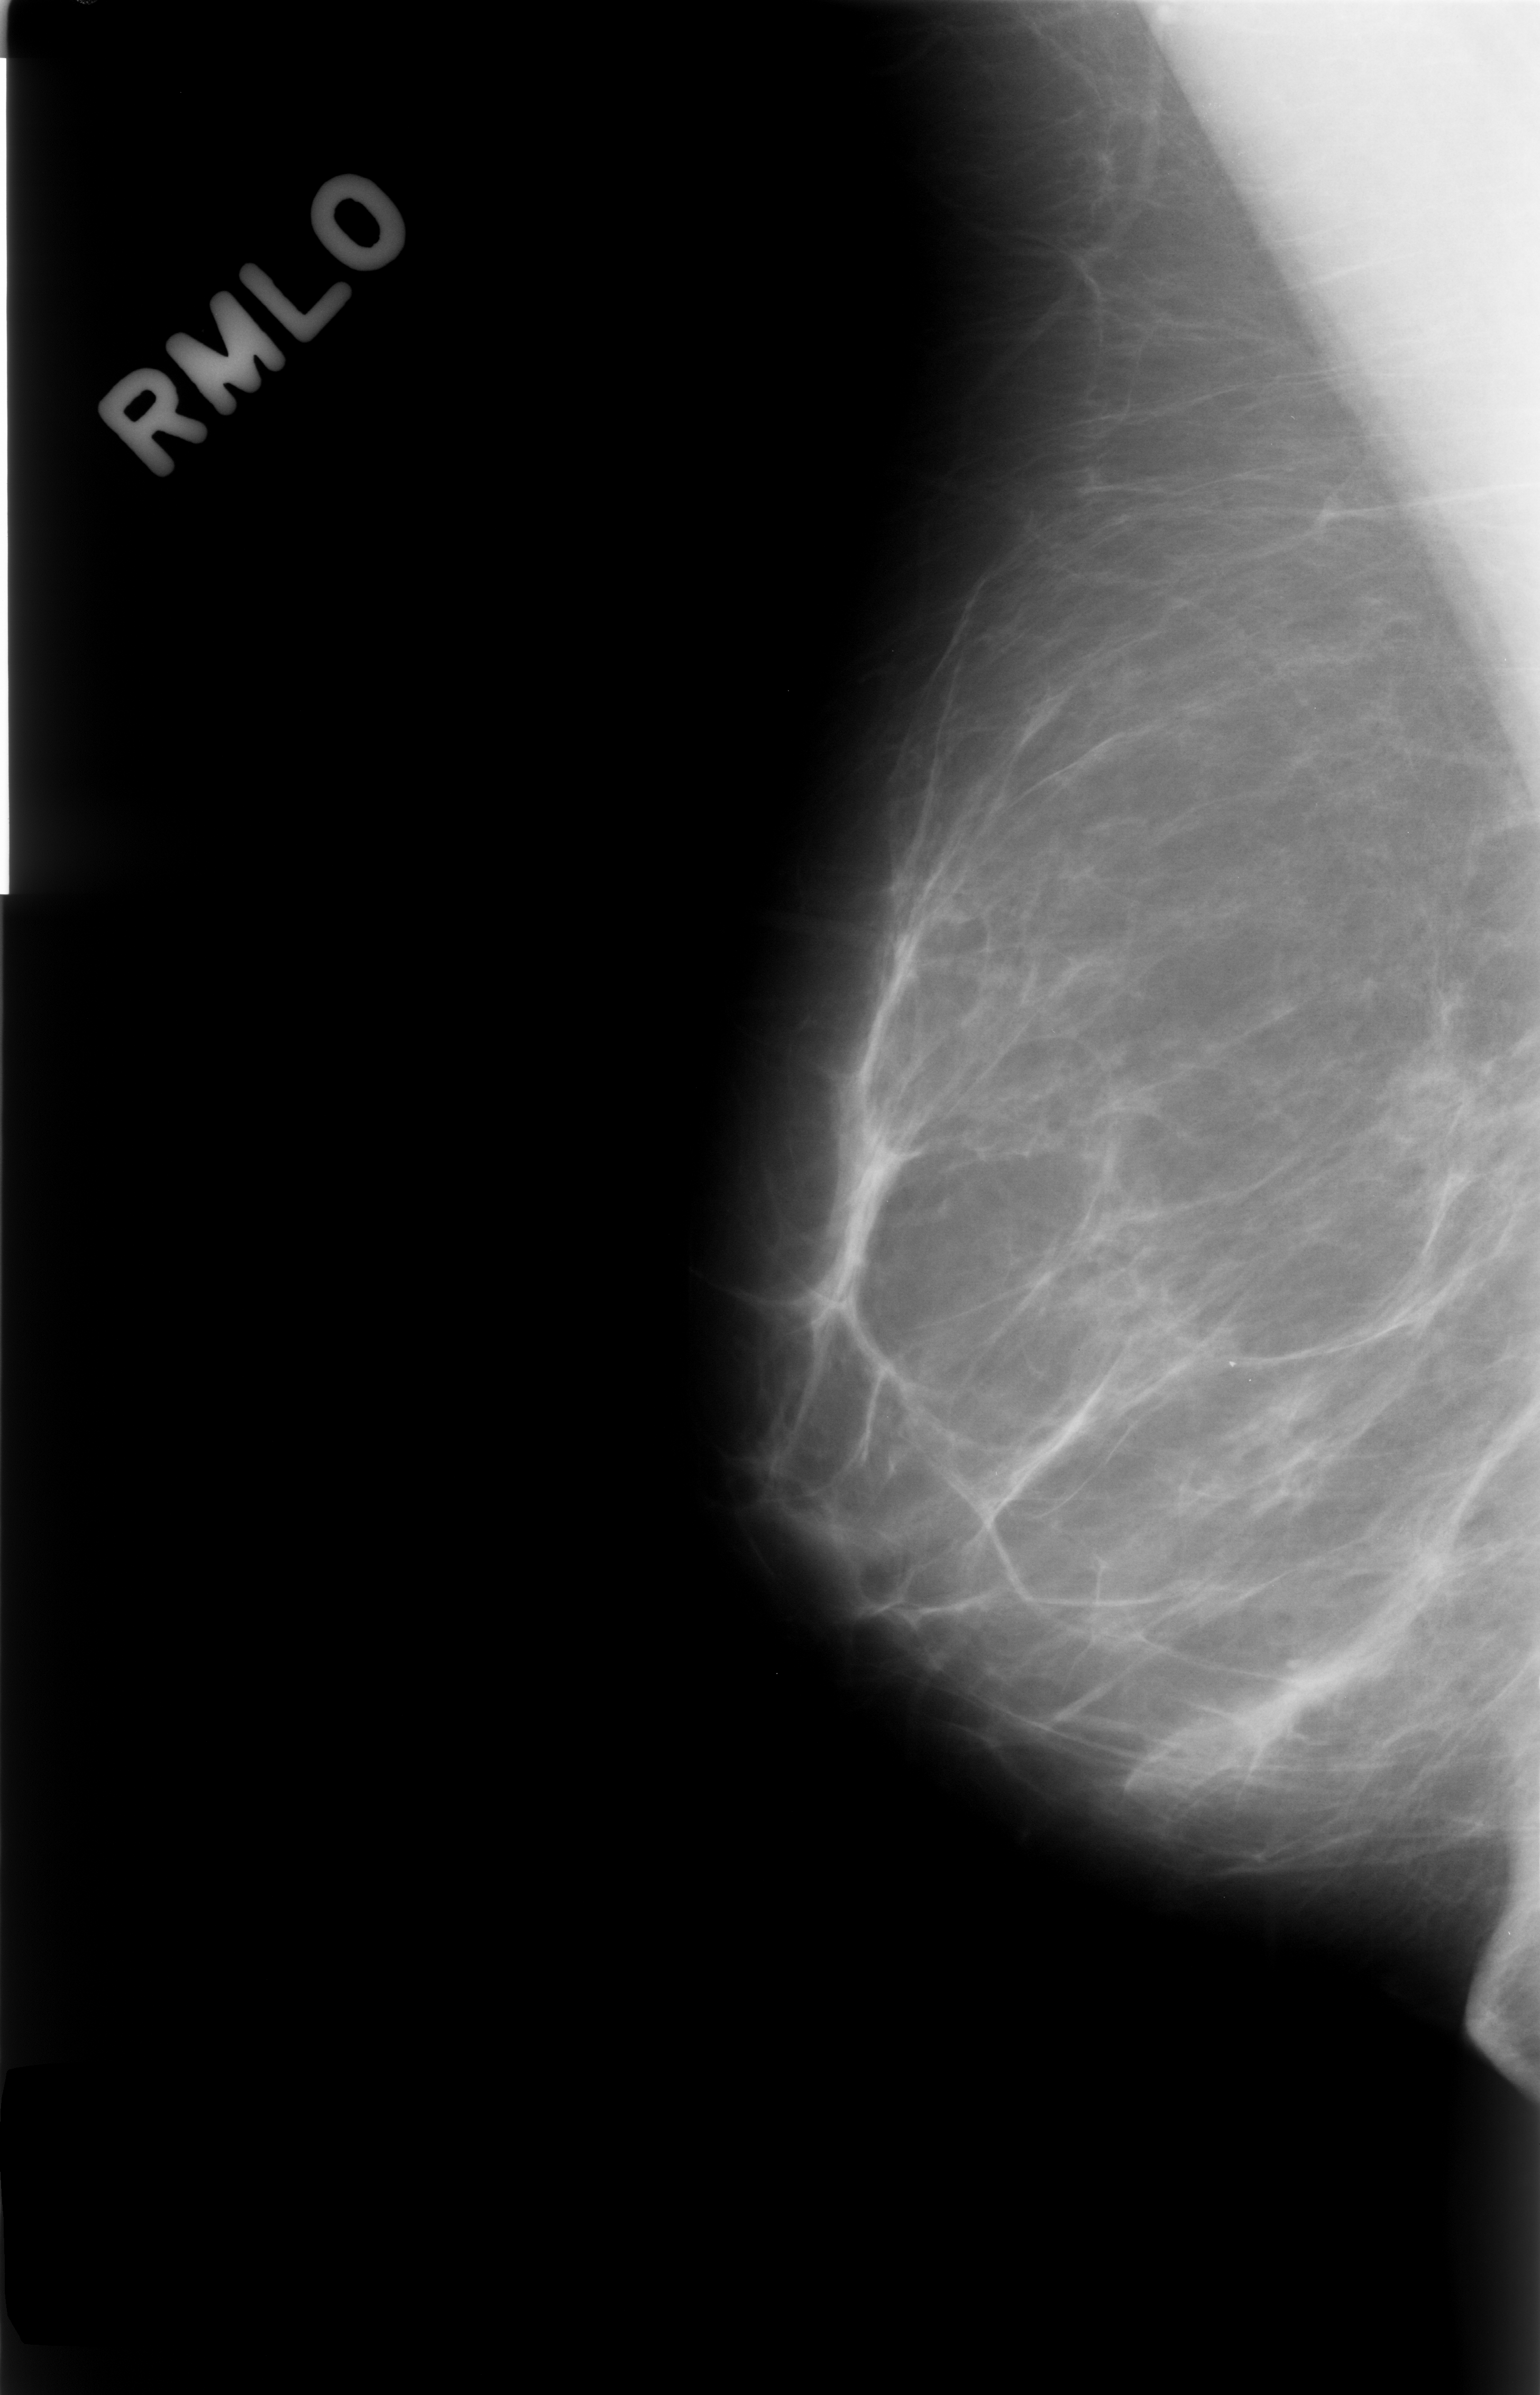
Digitized screen-film mammogram; right breast; MLO view; BI-RADS breast density category 1 (scale 1–4); 1540 × 2395 image matrix.
Marked abnormalities (boxes around the expert regions of interest):
- mass, shape focal asymmetric density; BI-RADS assessment category 3; benign; no additional work-up was recommended (outcome (as recorded, no biopsy): benign without callback): box from (x=1359, y=1004) to (x=1510, y=1227) px